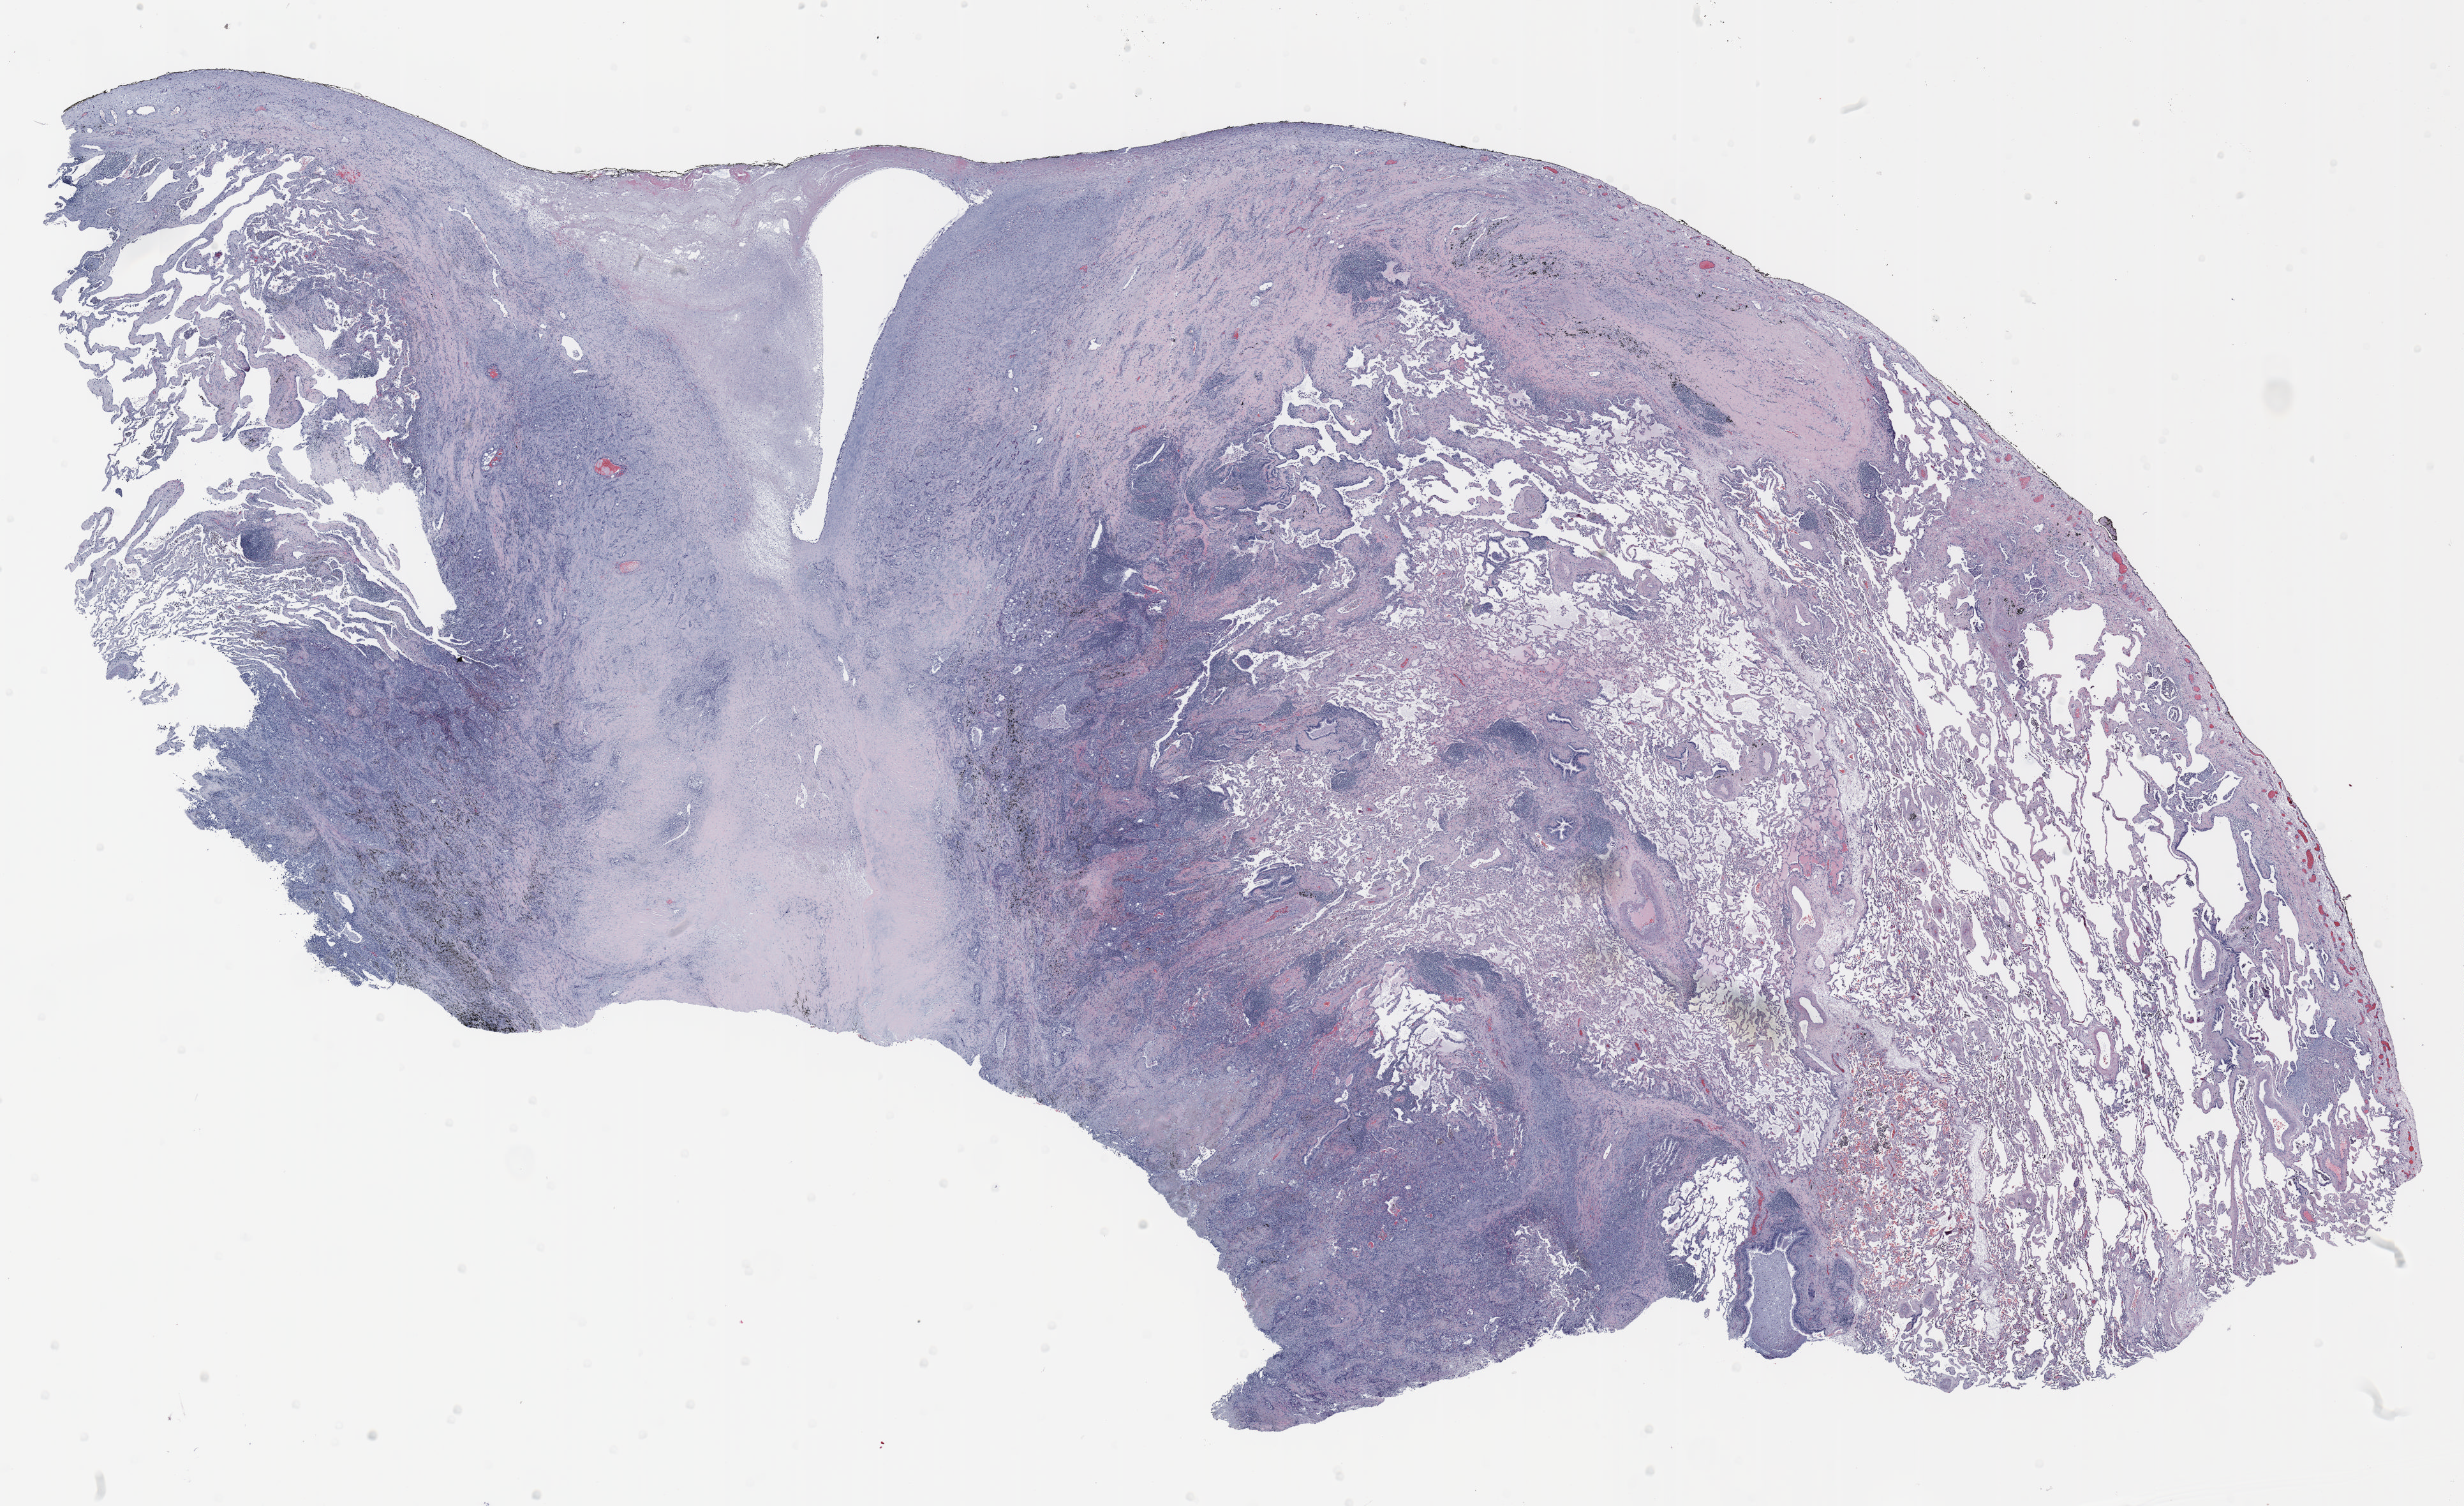
H&E whole-slide image — whole scanned area (about 31.0 x 19.0 mm, slide scanned at 20x) shown as a low-resolution overview, FFPE section, lung tissue. Male, age 71 at enrolment.
Participant's lung-cancer diagnosis: Squamous cell carcinoma, NOS.